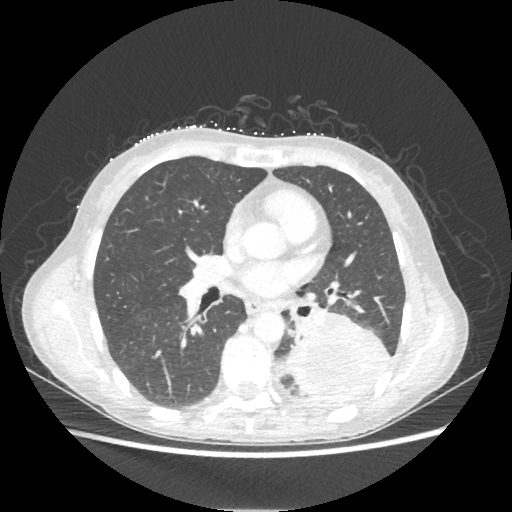
Chest CT, one axial slice. Position 116 of 221 along the scan axis. Reconstruction kernel STANDARD. Lung window (W 1500 / L -600 HU). 1.25 mm slice thickness. 512 × 512 image matrix, field of view 360 × 360 mm. Patient: female, 53 years. Case-level facts recorded for this patient, not image findings: clinical TNM (as recorded): T3 N0 M0.
Outlined on this slice (bounding box drawn by a radiologist):
- lung tumour (recorded histology: adenocarcinoma): bounding box [x1, y1, x2, y2] px = [289, 308, 391, 397]